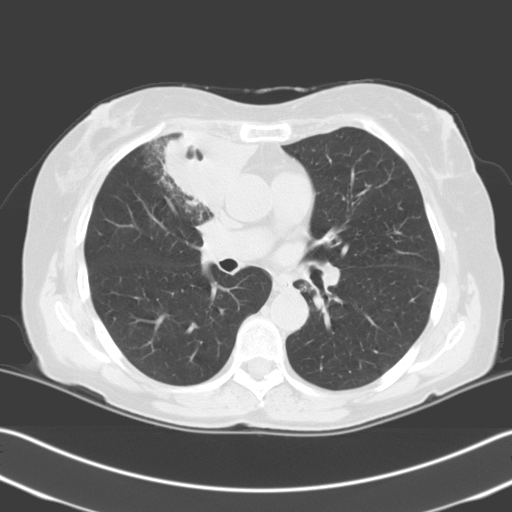
Low-dose screening chest CT, one axial slice; position 123 of 204 along the scan axis; 140 kVp; lung window (W 1500 / L -600 HU); 3.2 mm slice thickness; 512 × 512 image matrix.
Outlined on this slice (manually delineated by an expert):
- lesion 1 (tumor, upper lobe of right lung): box from (x=163, y=131) to (x=256, y=208) px